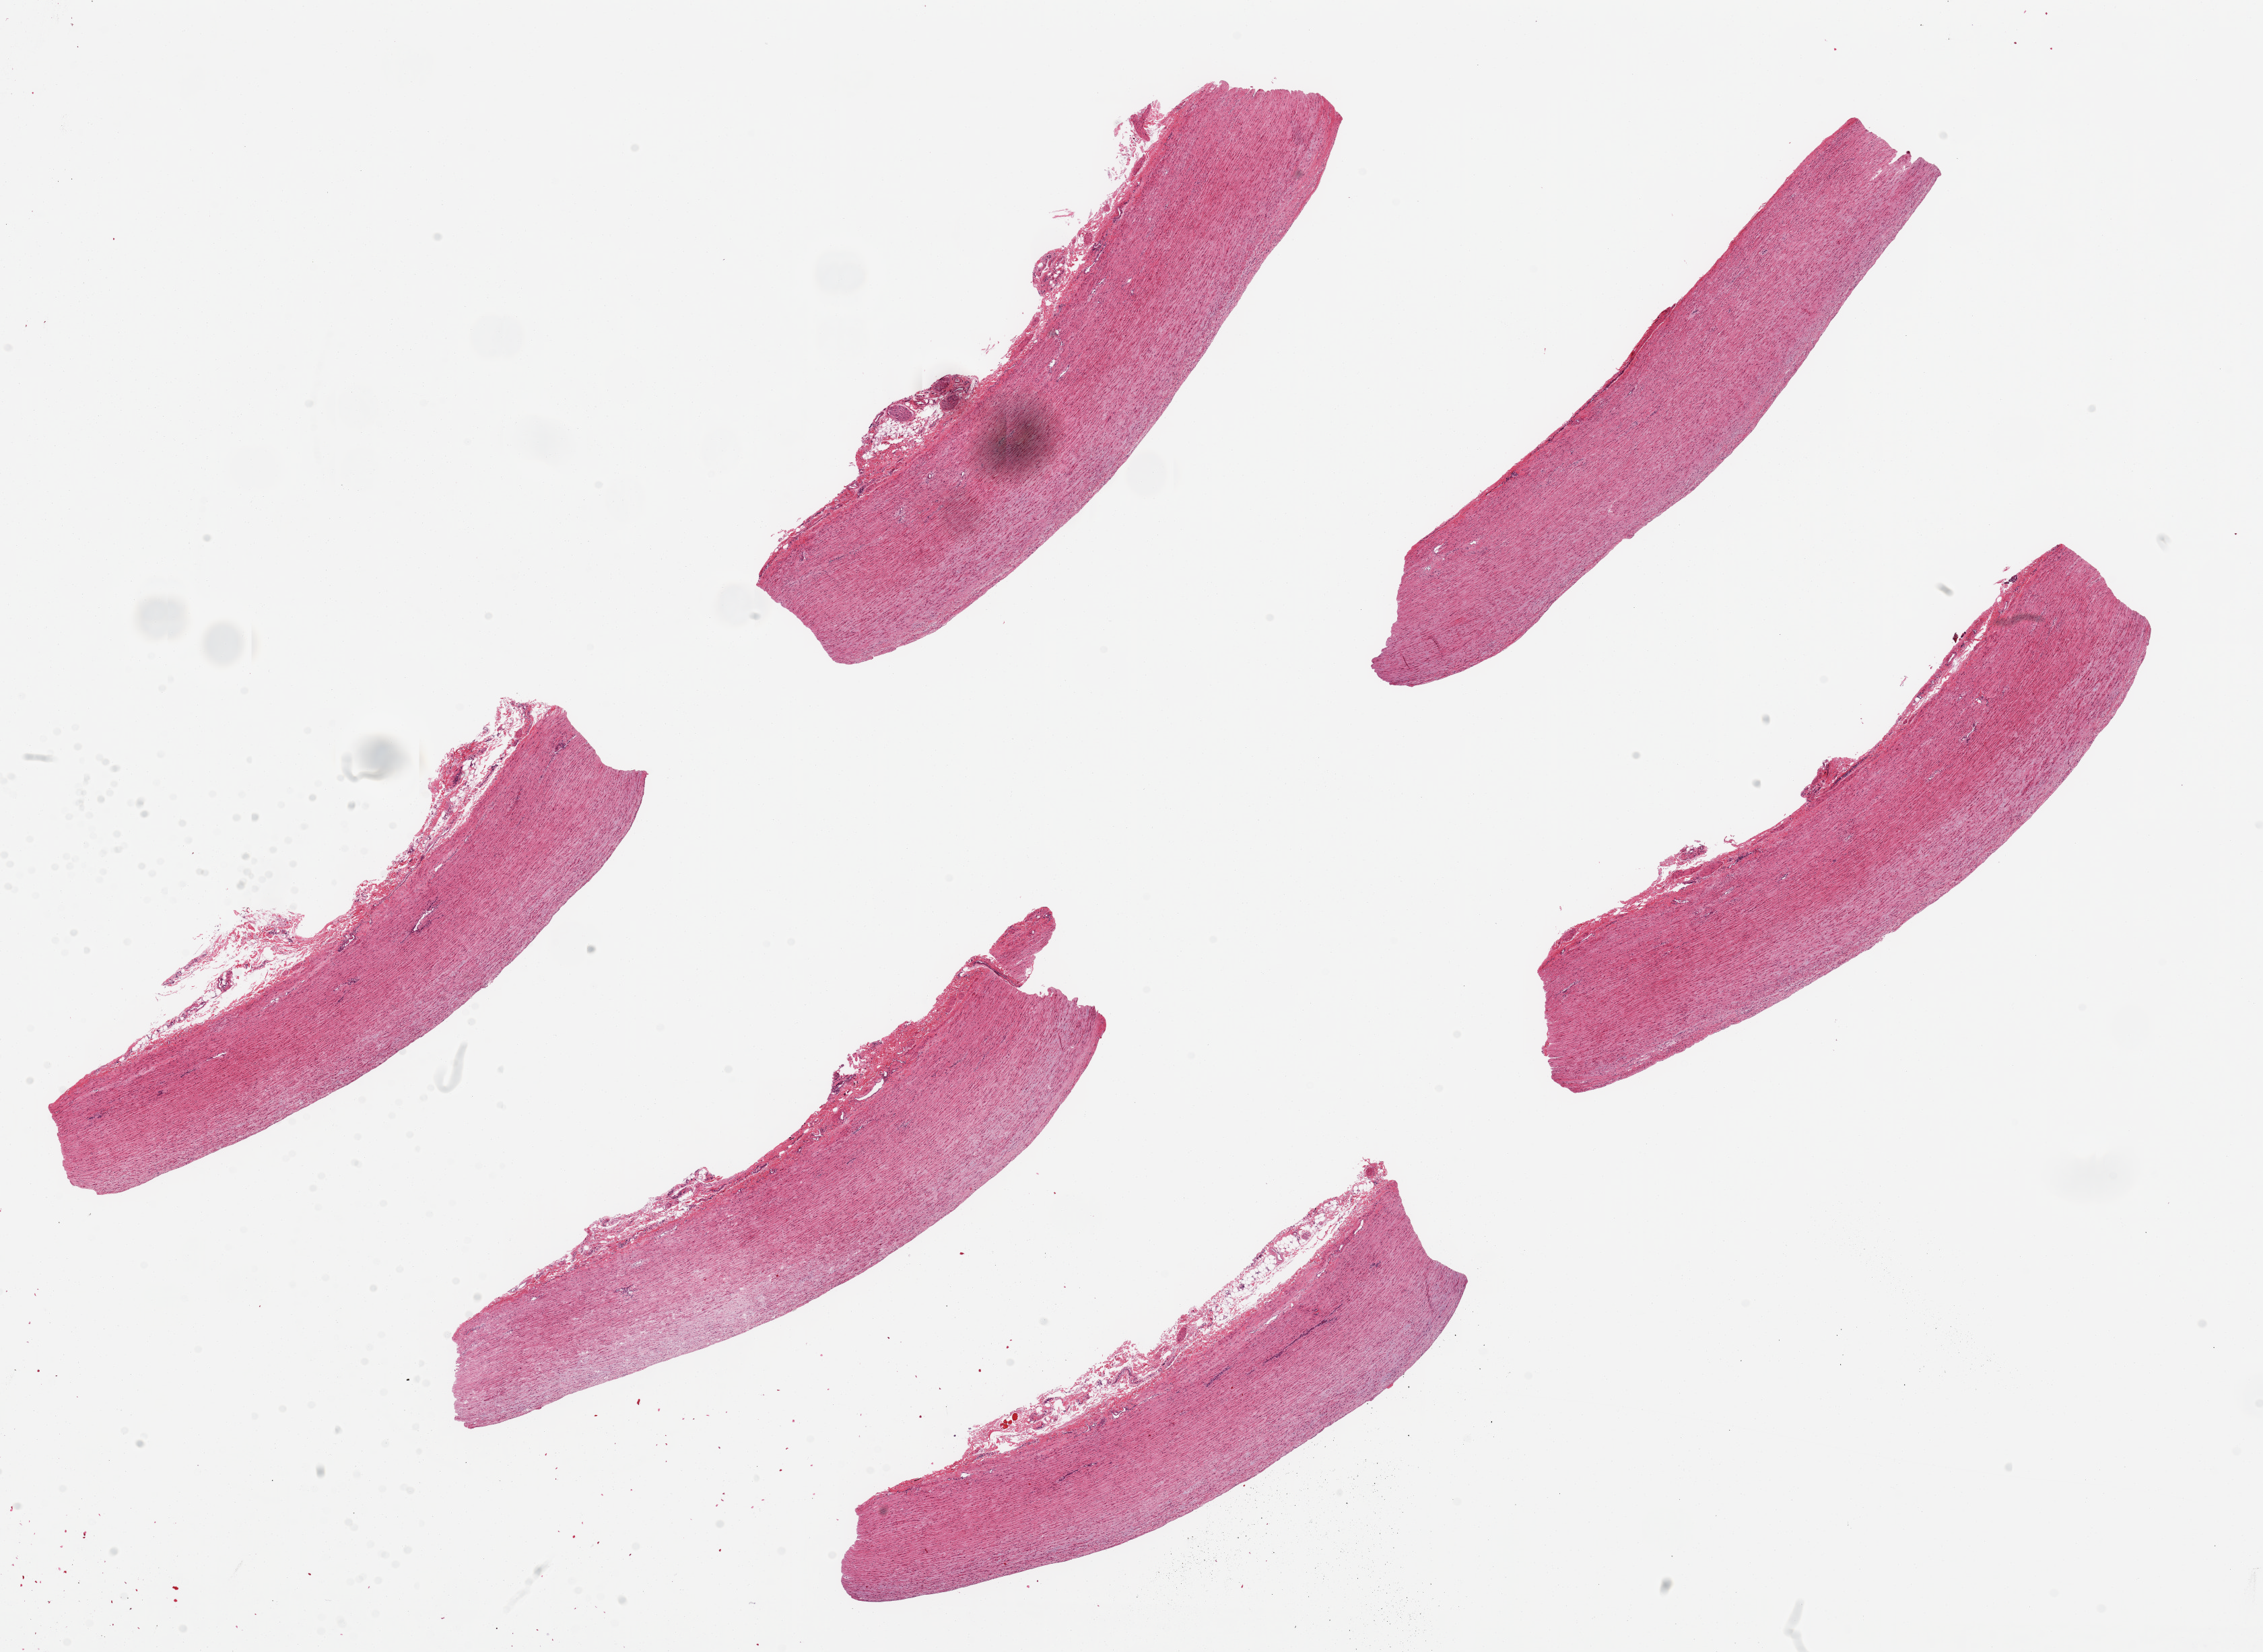
Haematoxylin and eosin whole-slide image — a low-resolution overview of the entire scanned area, about 26.6 x 19.4 mm. PAXgene-fixed, paraffin-embedded tissue. Section of aorta (target tissue). Tissue donor sample. Male donor.
Review note (as recorded): 6 ~ 8.5 x 2mm pieces.